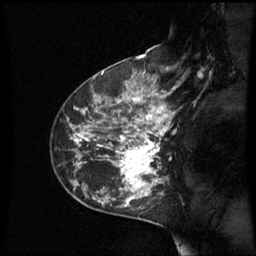
Breast MRI (dynamic contrast-enhanced), one sagittal slice; position 40 of 60 along the scan axis; dynamic contrast-enhanced series, image 2 of 3 at this slice position (ordered by acquisition); 1.5 T; TE 4.2 ms, TR 8.9 ms; 2.4 mm slice thickness; 256 × 256 image matrix, field of view 210 × 210 mm. Patient: female, 42 years. Case-level facts recorded for this patient, not image findings: setting: breast cancer imaged before/during neoadjuvant chemotherapy; receptor status: HER2-positive.
Annotated regions visible in this slice (semi-automatically segmented with operator editing):
- analysis volume of interest (the breast-tissue region the enhancement analysis was run in; not a lesion): box from (x=62, y=93) to (x=171, y=210) px
- tumour enhancement mask (voxels above the 70 % enhancement threshold inside the analysis volume of interest): (x=75, y=93)–(x=171, y=207)